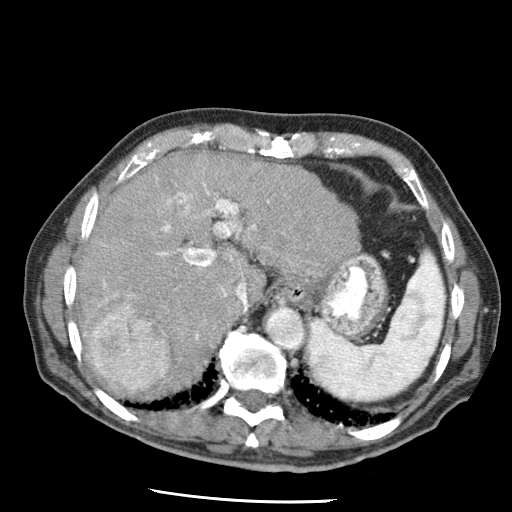
Contrast-enhanced abdominal CT (liver protocol), one axial slice; slice 49 of 79 in the series (ordered by position); 120 kVp; soft-tissue window (W 400 / L 40 HU); 2.5 mm slice thickness; 512 × 512 image matrix. Case-level facts recorded for this patient, not image findings: diagnosis: hepatocellular carcinoma (patient treated with transarterial chemoembolisation; whether this scan precedes or follows treatment is not stated here); TNM stage (as recorded): Stage-IIIA; Child-Pugh class: A; tumour nodularity: multinodular.
Structures marked on this image (semi-automatic segmentation, software-assisted and operator-edited):
- abdominal aorta: bounding box <266,308,304,348> (left, top, right, bottom; pixels)
- liver parenchyma outside the tumour (the mass and vessels are separate outlines, so this box may not span the whole liver): <69,152,358,393>
- mass: <90,303,169,388>
- liver vessels: <84,183,269,336>